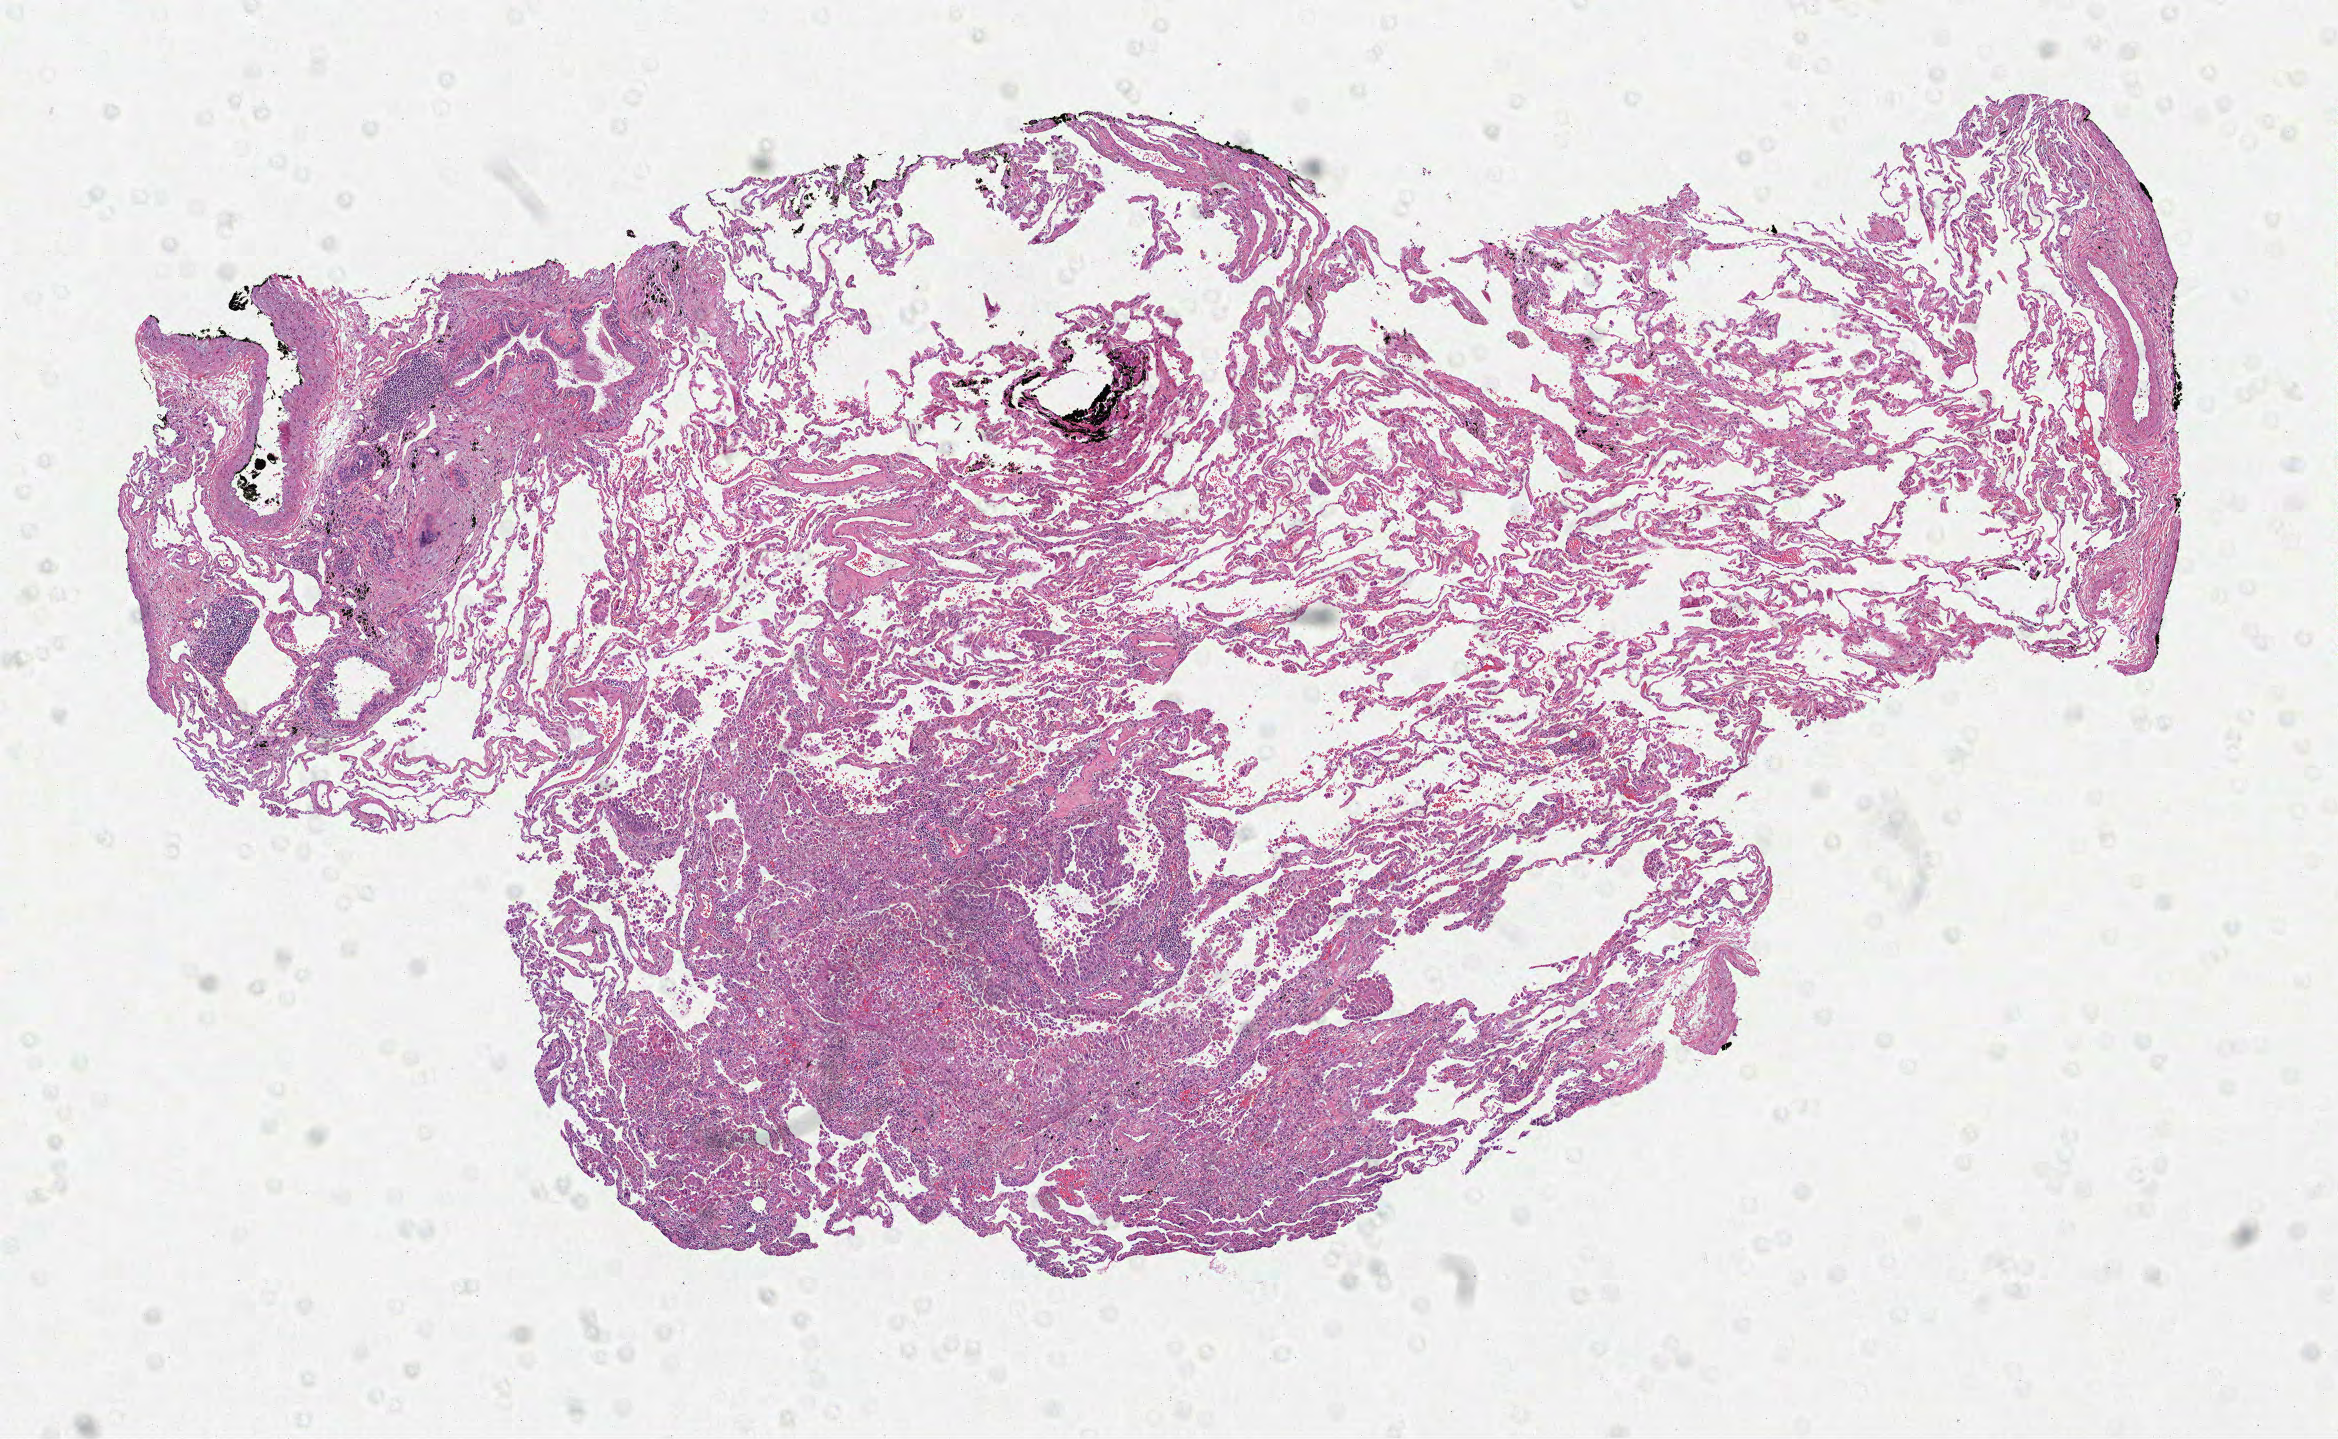
H&E-stained whole-slide image, a low-resolution overview of the entire scanned area, about 9.4 x 5.8 mm, formalin-fixed paraffin-embedded (FFPE) diagnostic section, sample: primary tumour, lung. Patient: female, age at initial diagnosis 76 years.
Pathologic diagnosis: Adenocarcinoma, NOS (upper lobe, lung).